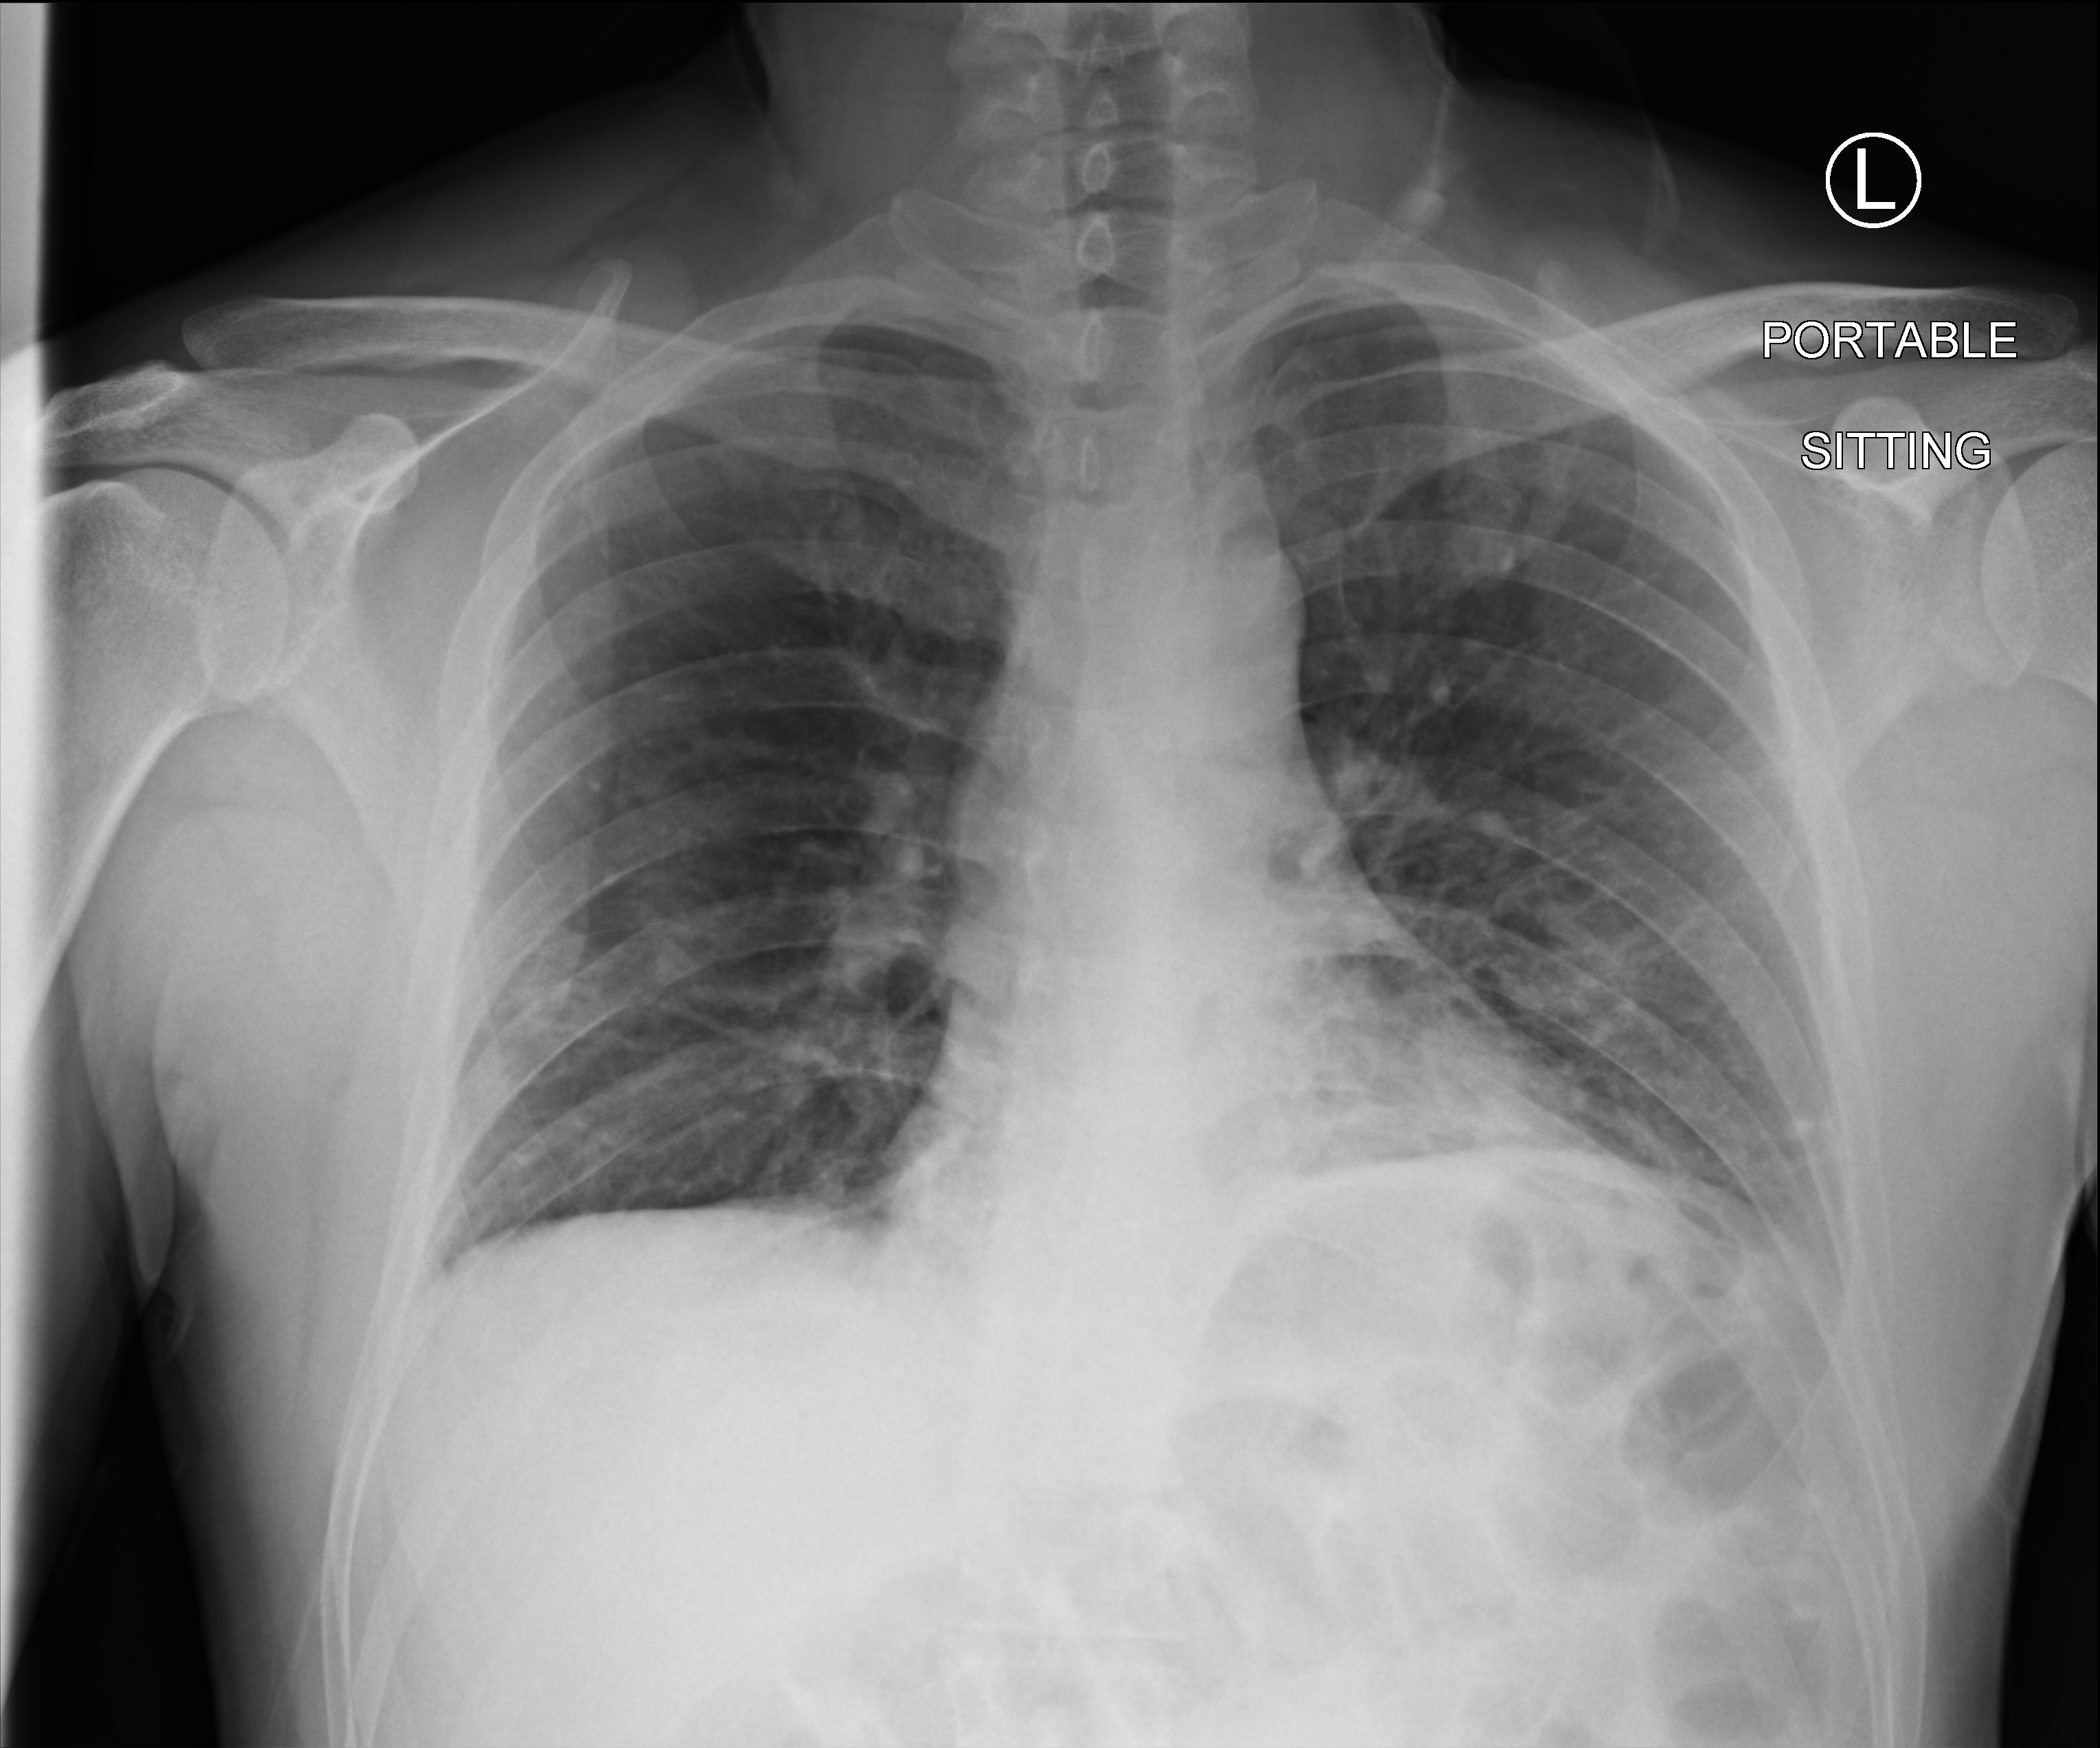
Chest X-ray (portable), anteroposterior (AP) projection. Patient hospitalised with COVID-19; male, aged 18–59 years.
From the hospital-stay record, not from the radiograph (when in the stay this image was taken is not recorded): mechanically ventilated during this hospital stay: no; admitted to intensive care during this hospital stay: no.